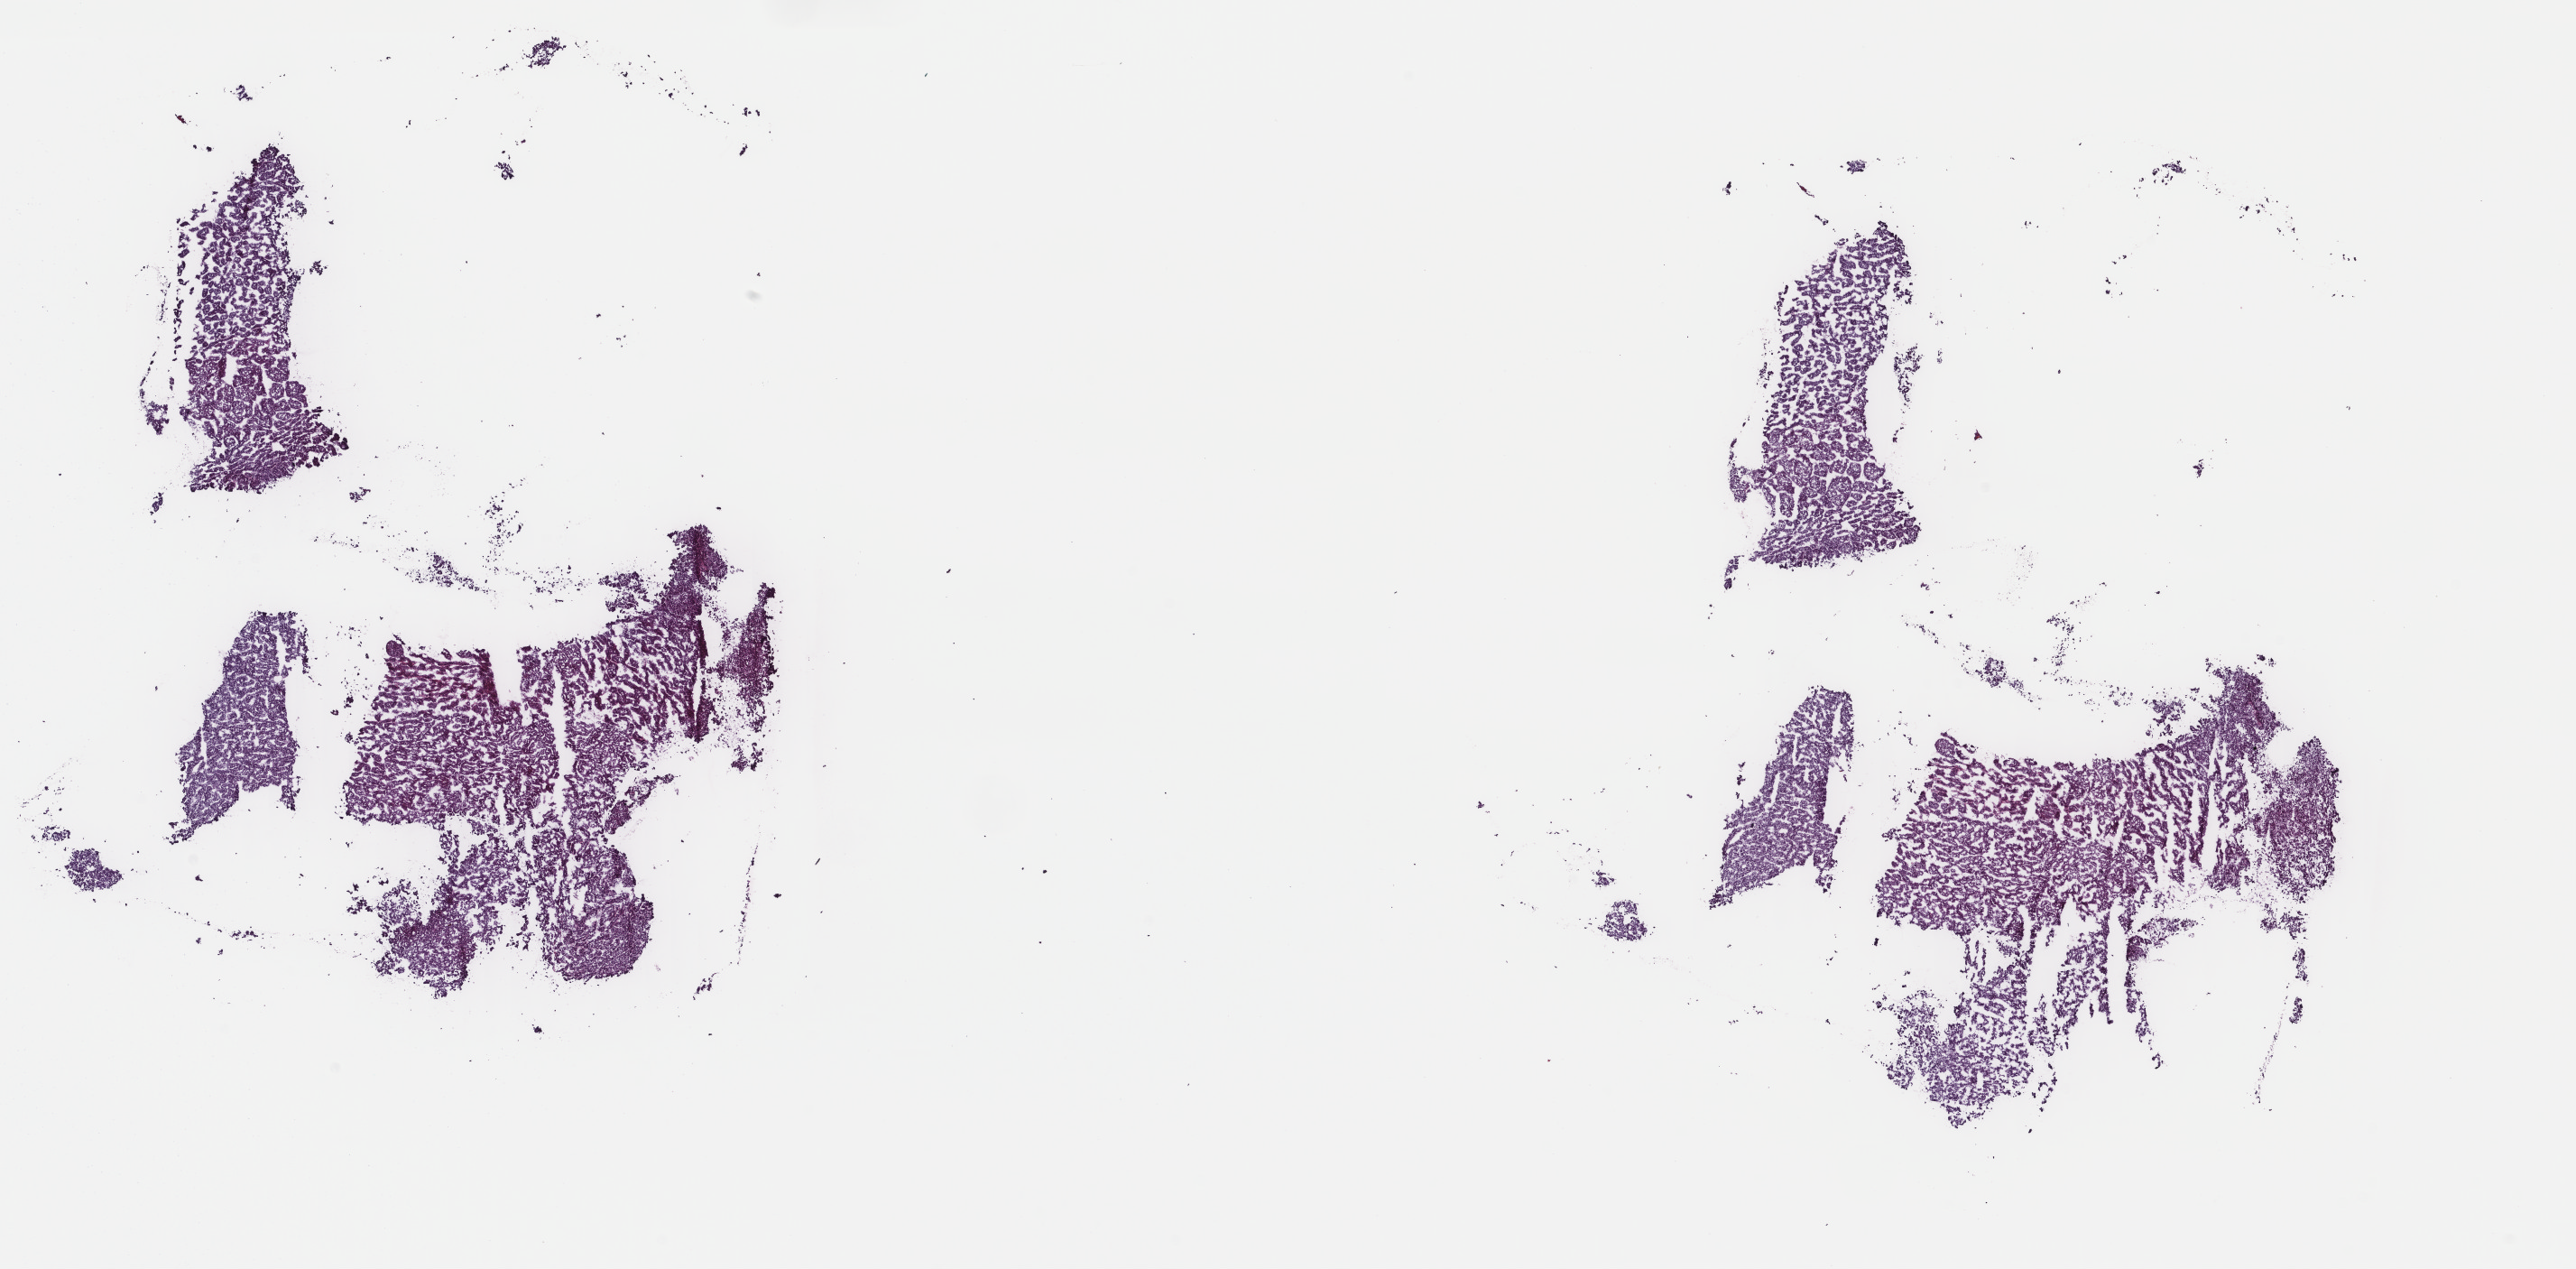
Digitized H&E tissue section (whole slide), whole scanned area (about 22.7 x 11.2 mm, slide scanned at 40x) shown as a low-resolution overview, frozen section from the top of the tissue portion, liver, primary tumour sample. Female, age 43 years at initial diagnosis. Histologic grade: G2 (moderately differentiated). Pathologist review of this section (percent, as recorded): tumour cells 100%, tumour nuclei 90%, normal cells 0%, stromal cells 0%, necrosis 0%. Inflammatory infiltration, as recorded: lymphocyte infiltration 1%, monocyte infiltration 0%, neutrophil infiltration 0%.
- AJCC pathologic stage: II (4th edition)
- pathologic diagnosis: Hepatocellular carcinoma, NOS